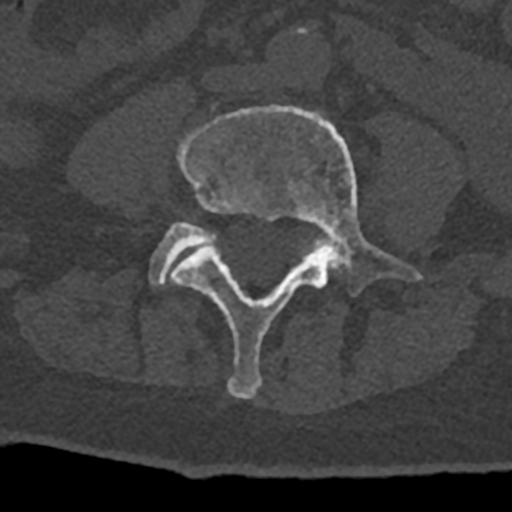
CT including the spine, one axial slice. Slice 247 of 797 in the series (ordered by position). Reconstruction kernel Br40s/3. 120 kVp. Bone window (W 1800 / L 400 HU). 0.5 mm slice thickness. 512 × 512 image matrix, field of view 160 × 160 mm. Male patient, age 74 years. From the clinical record (not read from this slice): primary cancer: renal.
Structures marked on this image (semi-automatic segmentation, software-assisted and operator-edited):
- L4 vertebra: box from (x=170, y=105) to (x=423, y=399) px
- L5 vertebra: (x=149, y=222)–(x=320, y=286)